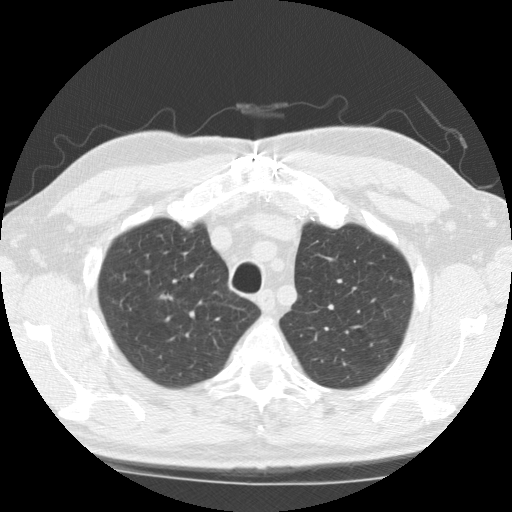
Low-dose screening chest CT, one axial slice. Slice 153 of 196 in the series (ordered by position). Reconstruction kernel STANDARD. 120 kVp. Lung window (W 1500 / L -600 HU). 2.5 mm slice thickness. 512 × 512 image matrix.
Annotated regions visible in this slice (outlined manually by an expert reader):
- lesion 1 (tumor, upper lobe of right lung): bounding box [x1, y1, x2, y2] px = [155, 343, 169, 353]